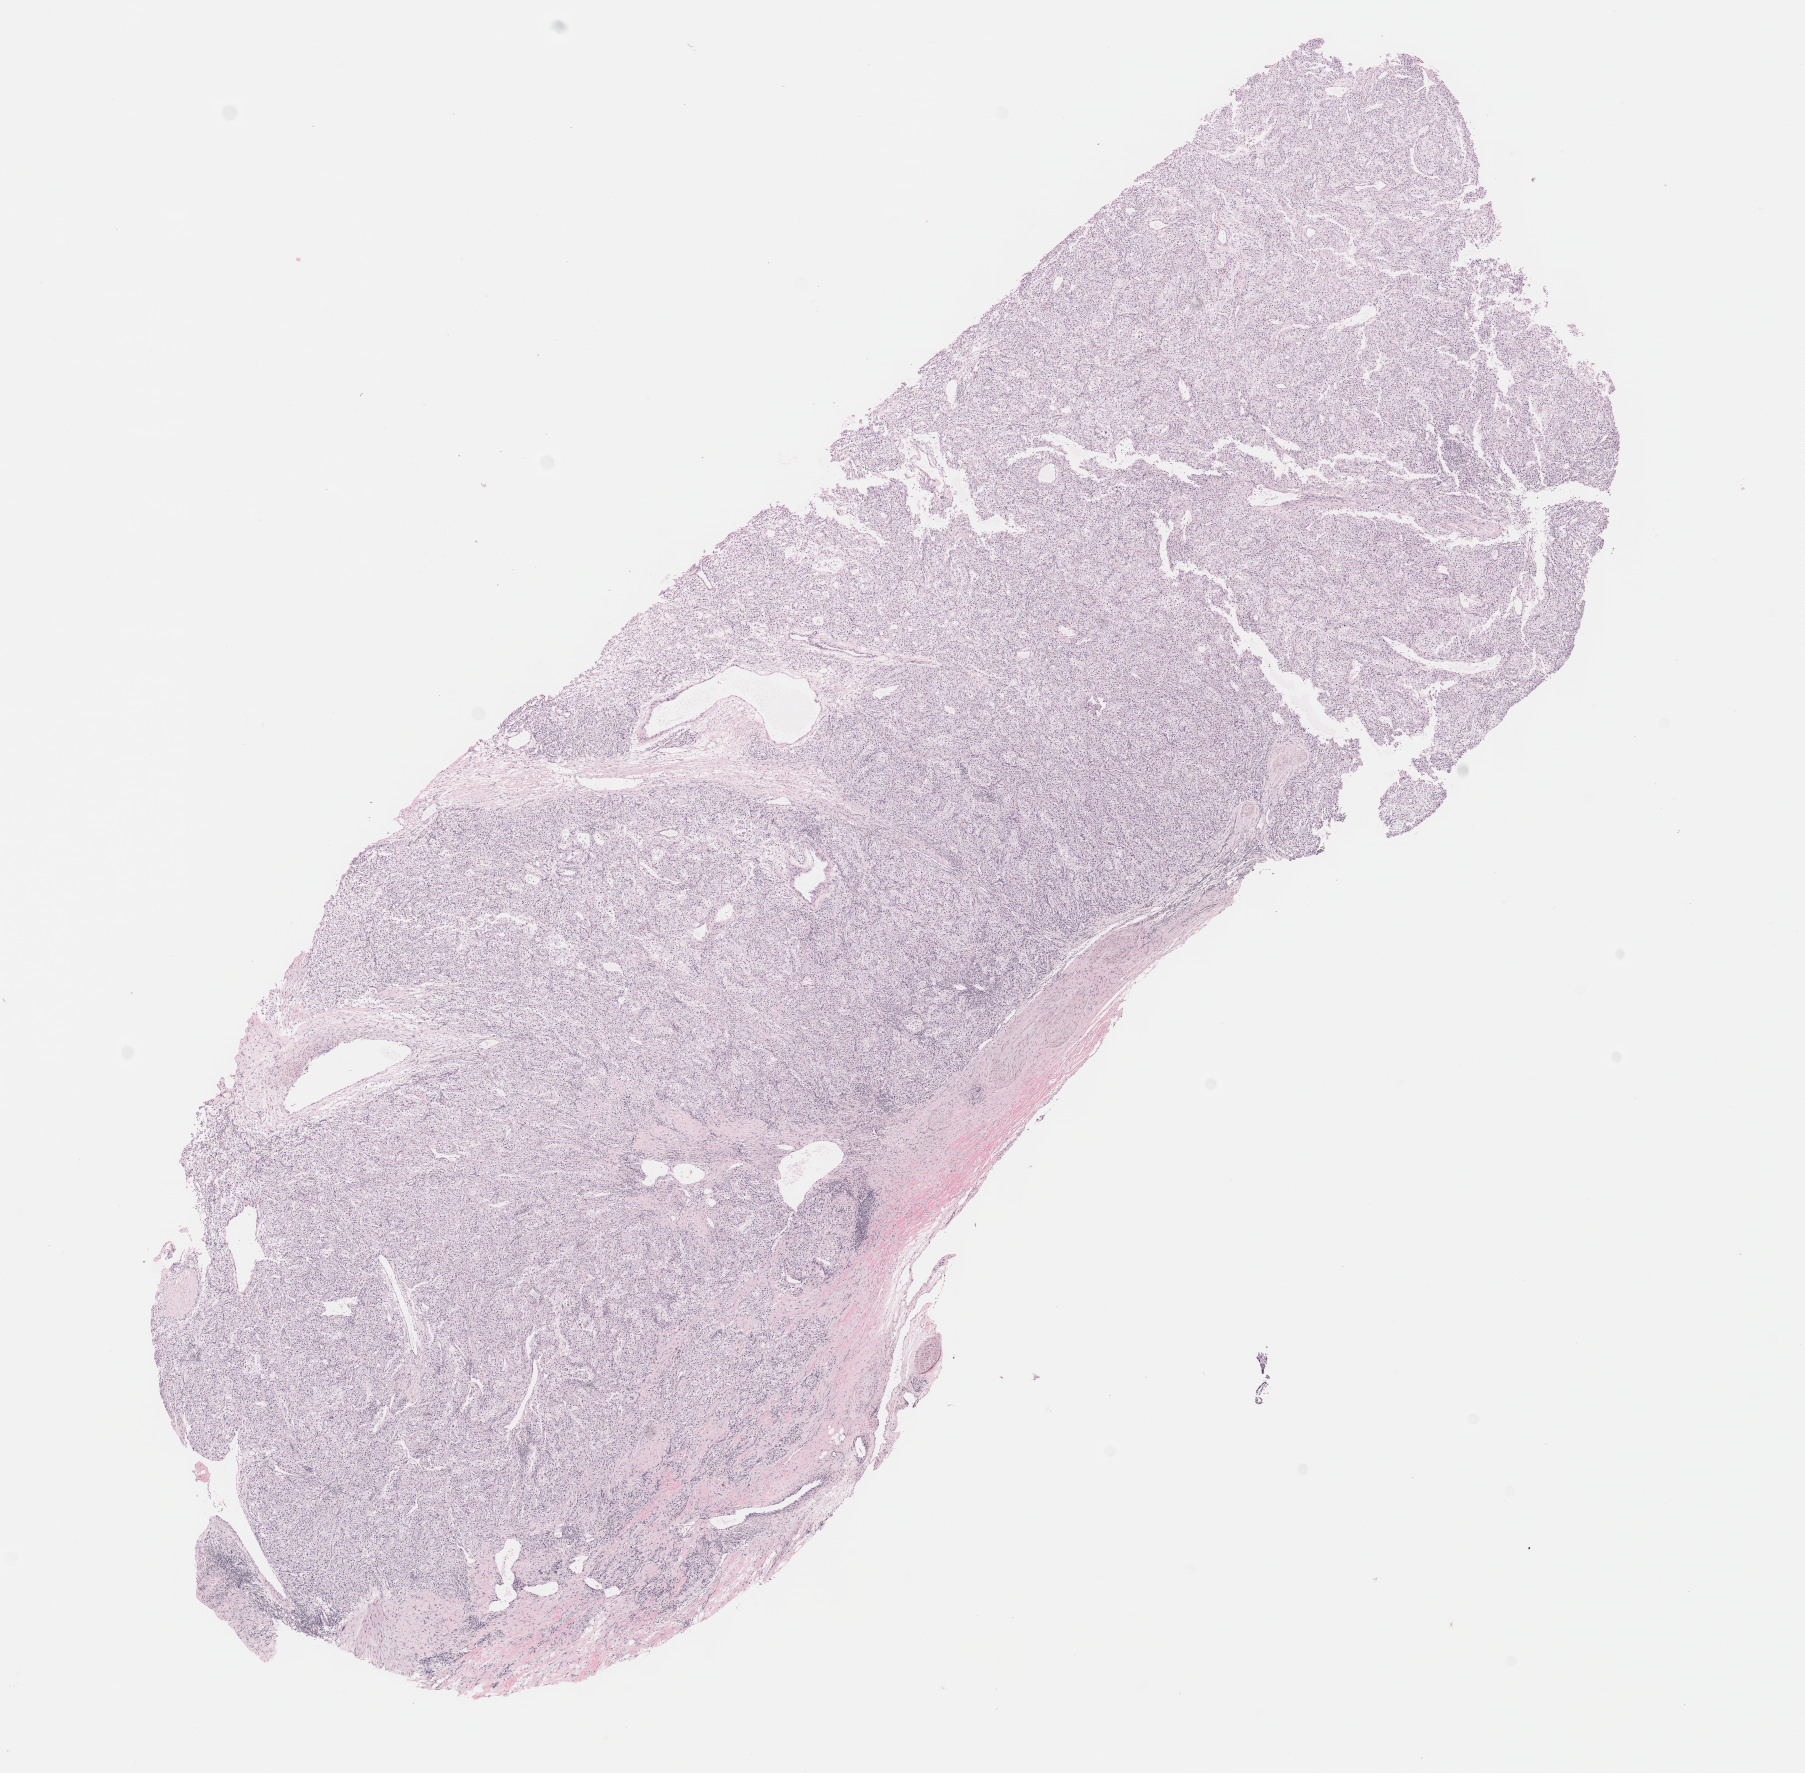
H&E-stained whole-slide image, whole scanned area (about 14.6 x 14.3 mm, slide scanned at 40x) shown as a low-resolution overview; formalin-fixed paraffin-embedded (FFPE) diagnostic section; sample: primary tumour, kidney. Male patient; age at initial diagnosis 40 years.
Pathologic diagnosis: Clear cell adenocarcinoma, NOS.